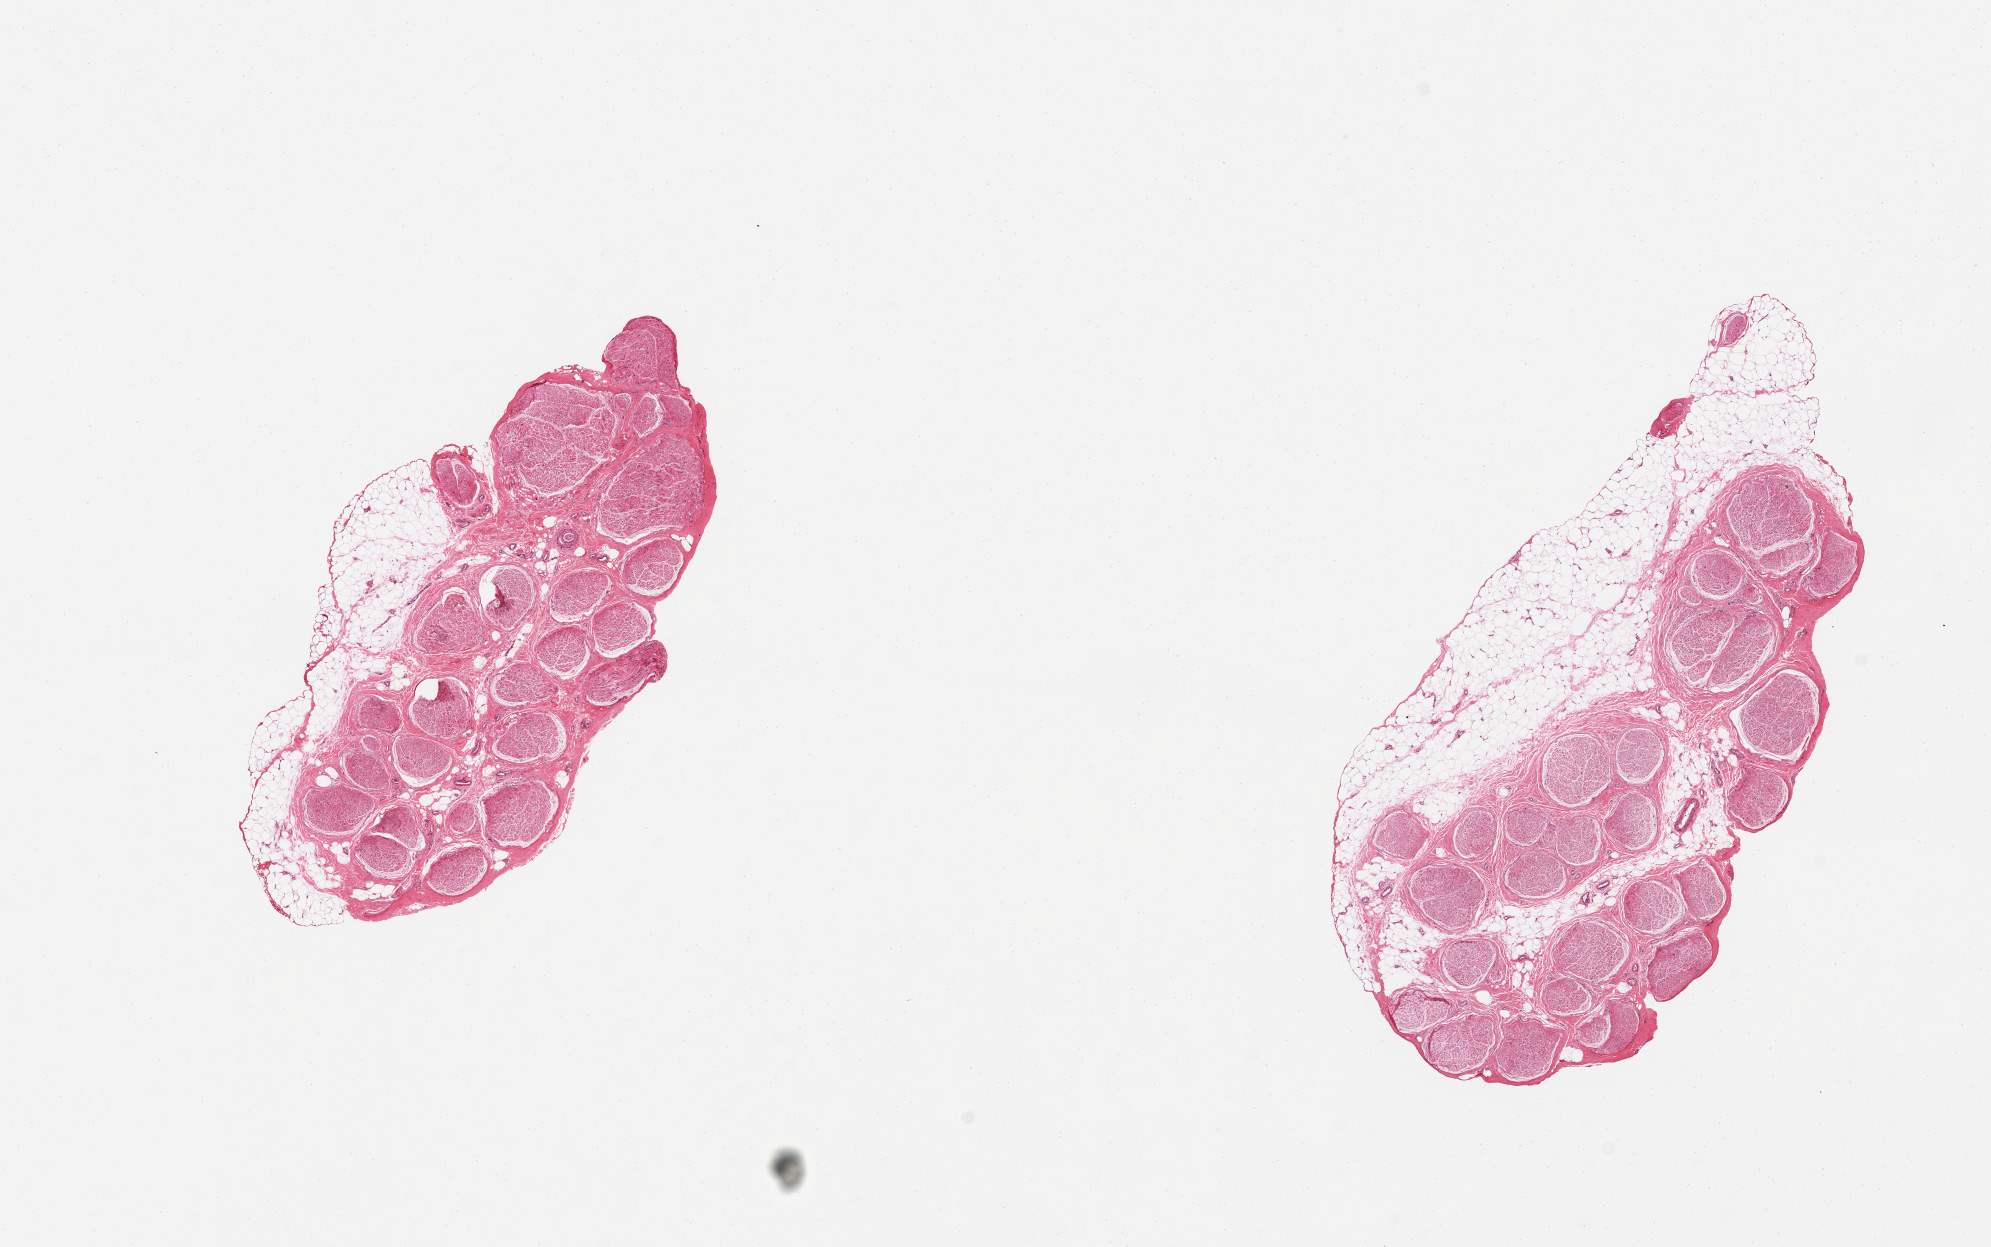
Hematoxylin and eosin (H&E) whole-slide image, brightfield, low-resolution overview of the scanned area, about 15.8 x 9.9 mm. PAXgene-fixed, paraffin-embedded tissue. Sampled site (target tissue): tibial nerve. Donor tissue sample. Donor: female.
Reviewer comment on this tissue sample: 2 pieces, both with 20-30% attached fat.